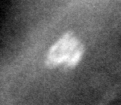
Region of interest cut from a scanned film mammogram (one marked finding), right breast, MLO view.
Calcifications, morphology lucent center; BI-RADS assessment category 2; subtlety rating 5 on a 1 (subtle) to 5 (obvious) scale; benign; no additional work-up was recommended (benign without callback).